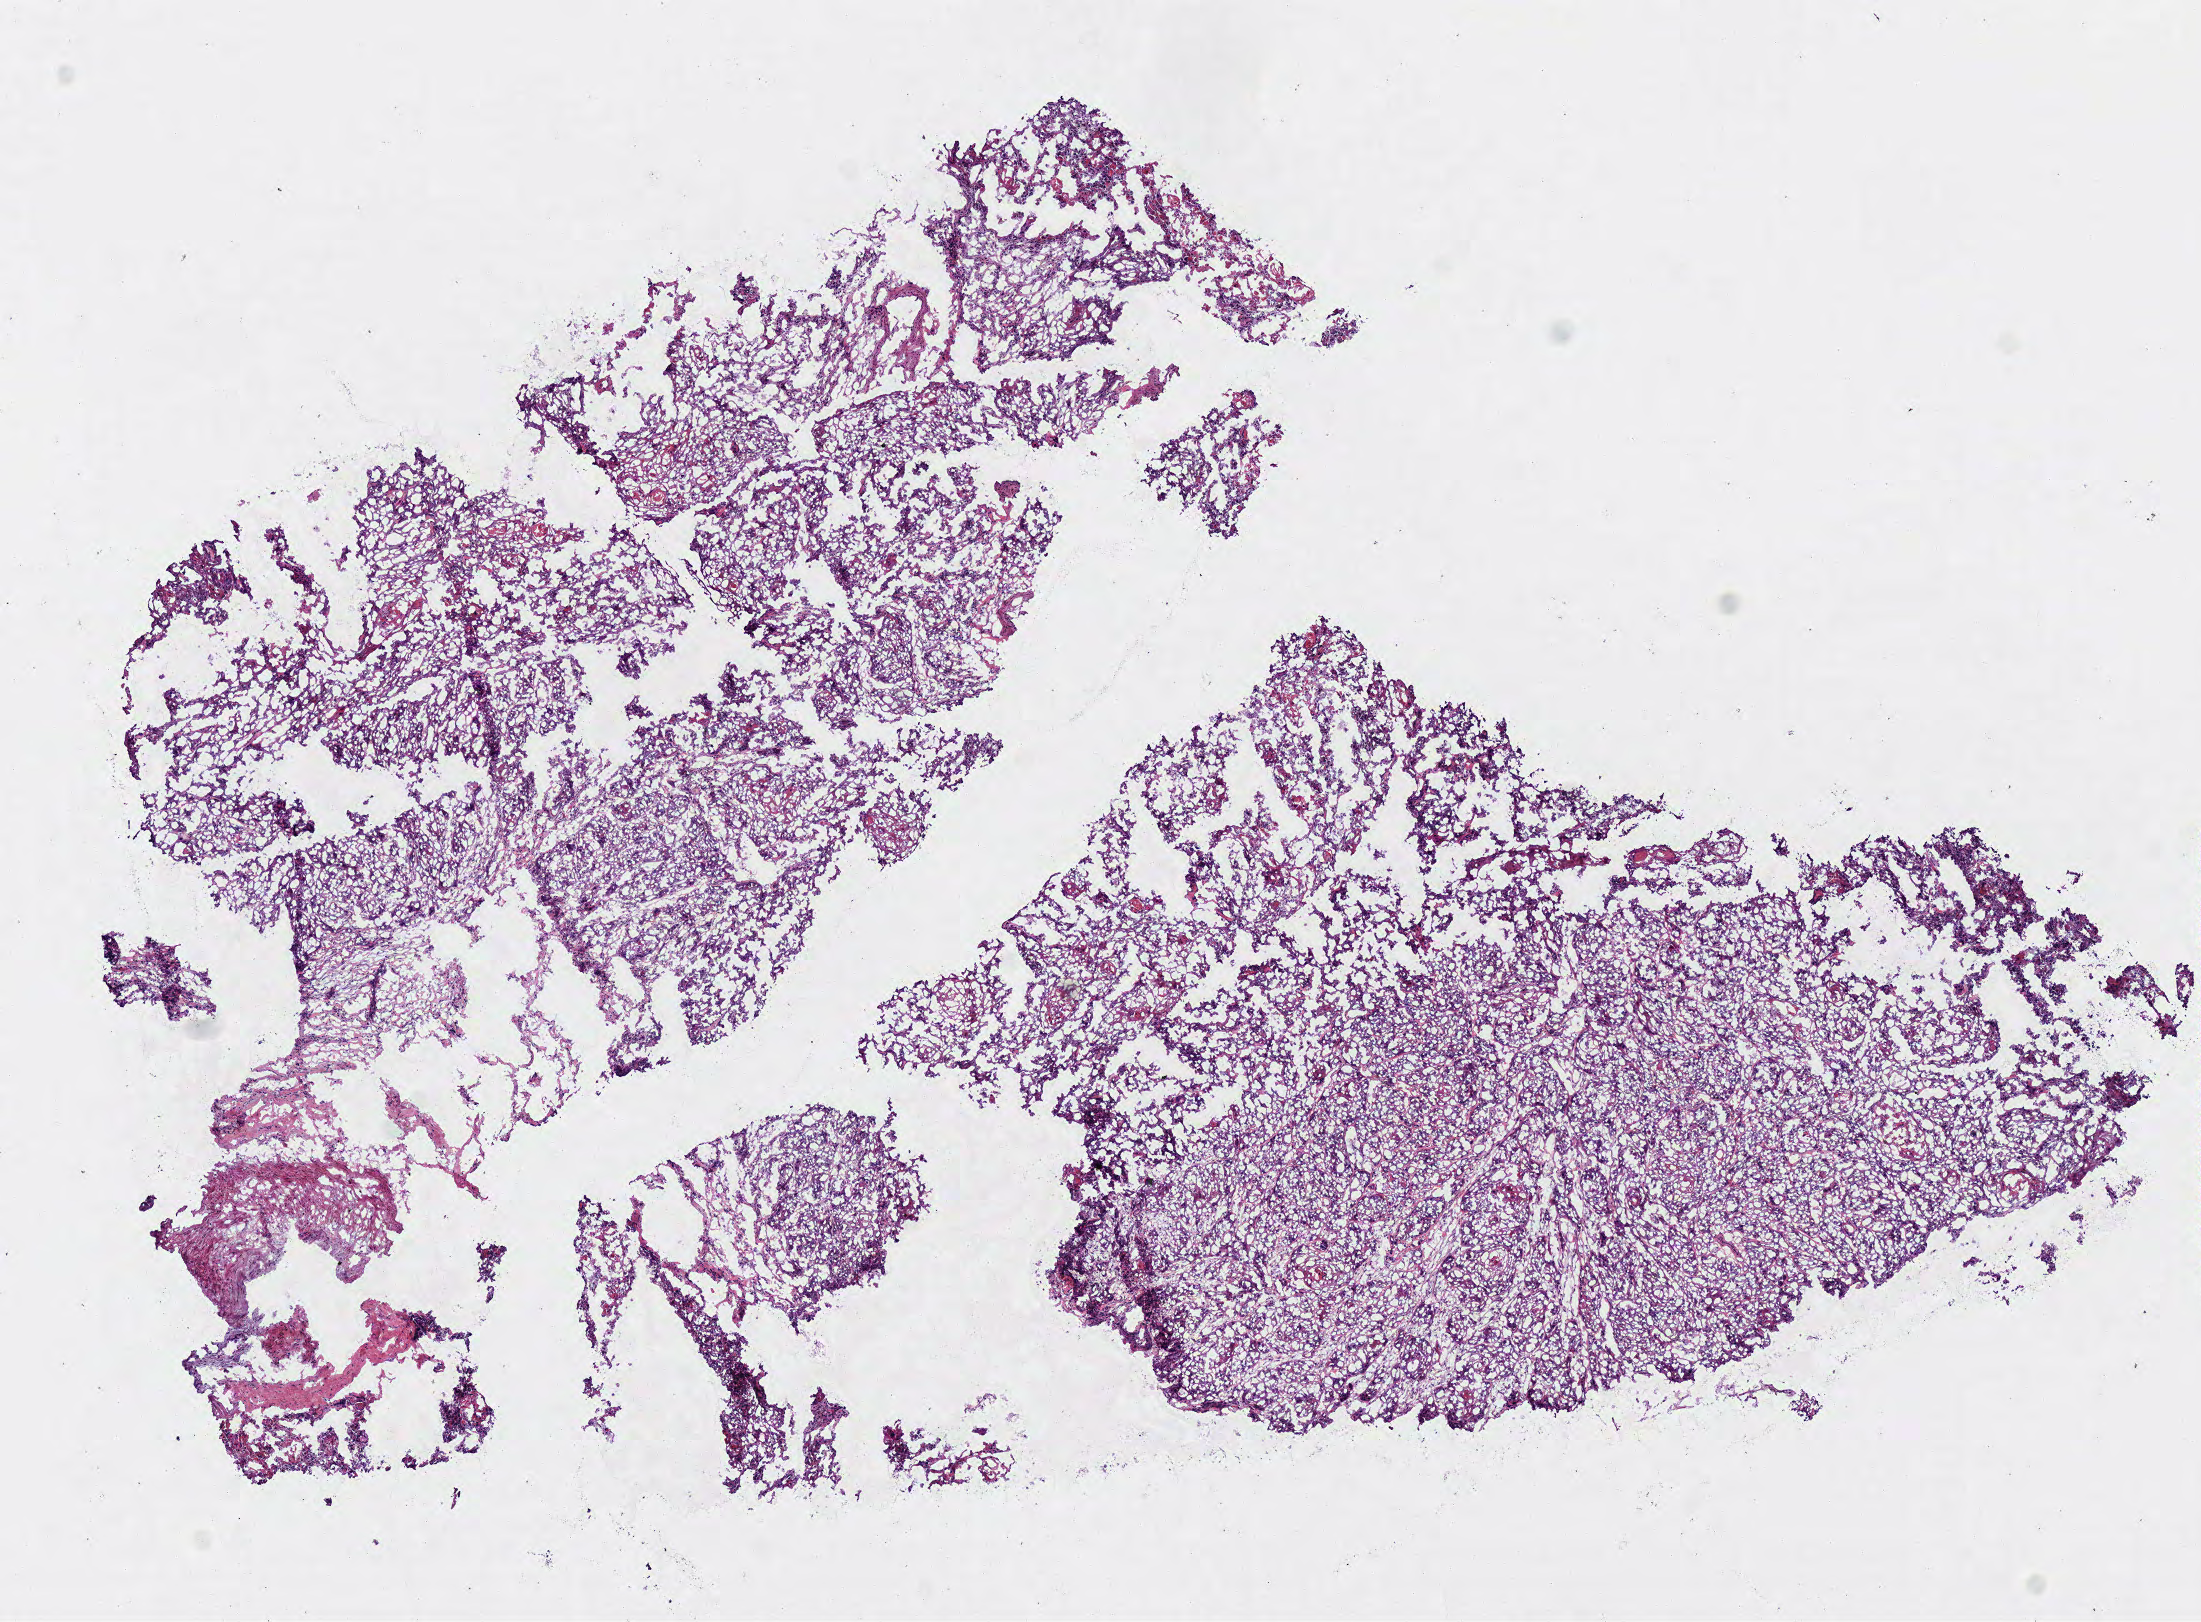
H&E-stained whole-slide image — shown as a low-resolution overview of the whole scanned area (about 8.7 x 6.4 mm, from a 40x scan); frozen section from the bottom of the tissue portion; sample: primary tumour, head and neck. Male patient; age at initial diagnosis 50 years. Histologic grade: G2 (moderately differentiated). Slide review estimates, as recorded: tumour cells 90%, tumour nuclei 85%, normal cells 0%, stromal cells 10%, necrosis 0%.
Pathologic diagnosis: Squamous cell carcinoma, NOS (tongue, NOS). Lymph nodes positive (case pathology): 2 of 50 examined. AJCC pathologic stage: IVA.